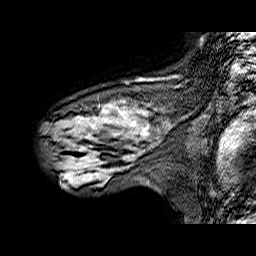
Breast MRI (dynamic contrast-enhanced), one sagittal slice. Dynamic contrast-enhanced series, time point 2 of 6 at this slice position (early post-contrast). 1.5 T. TE 6.3 ms, TR 32.9 ms. 4 mm slice thickness. 256 × 256 image matrix, field of view 200 × 200 mm. Female patient. Case-level facts recorded for this patient, not image findings: setting: breast cancer imaged before/during neoadjuvant chemotherapy; receptor status: HER2-positive.
Annotated regions visible in this slice (semi-automatic segmentation, software-assisted and operator-edited):
- analysis volume of interest (the breast-tissue region the enhancement analysis was run in; not a lesion): bounding box <44,86,174,173> (left, top, right, bottom; pixels)
- tumour enhancement mask (voxels above the 100 % enhancement threshold inside the analysis volume of interest): <104,110,147,135>